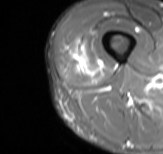
MRI of an extremity soft-tissue mass, one axial slice. Slice 14 of 61 in the series (ordered by position). STIR. MR volume resampled by the dataset authors to the PET/CT grid (not the native acquisition matrix). 163 × 154 image matrix, field of view 159 × 150 mm. Male patient. Case-level facts recorded for this patient, not image findings: histological type: poorly differentiated synovial sarcoma; grade: high; site of the primary tumour: right buttock.
Annotated regions visible in this slice (expert contour drawn on MRI and transferred to this co-registered scan by the dataset authors):
- gross tumour volume including surrounding oedema: bounding box (x1, y1, x2, y2) in pixels: (69, 41, 101, 76)